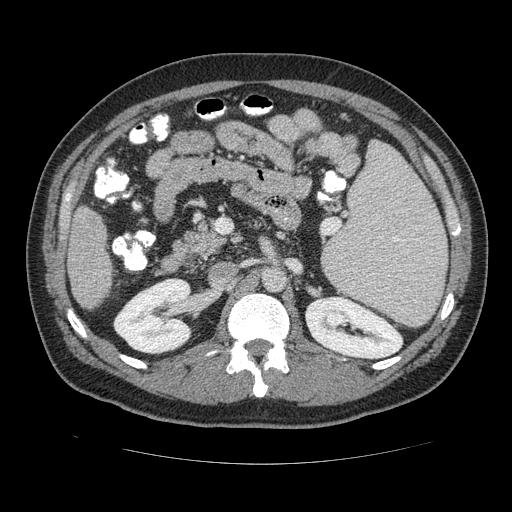
Contrast-enhanced abdominal CT (liver protocol), one axial slice. Position 56 of 113 along the scan axis. 120 kVp. Soft-tissue window (W 400 / L 40 HU). 2.5 mm slice thickness. 512 × 512 image matrix, field of view 400 × 400 mm. From the clinical record (not read from this slice): diagnosis: hepatocellular carcinoma (patient treated with transarterial chemoembolisation; whether this scan precedes or follows treatment is not stated here); TNM stage (as recorded): Stage-II; Child-Pugh class: B.
Outlined on this slice (semi-automatically segmented with operator editing):
- liver parenchyma outside the tumour (the mass and vessels are separate outlines, so this box may not span the whole liver): bounding box (x1, y1, x2, y2) in pixels: (64, 202, 114, 312)
- liver vessels: (97, 278, 102, 282)